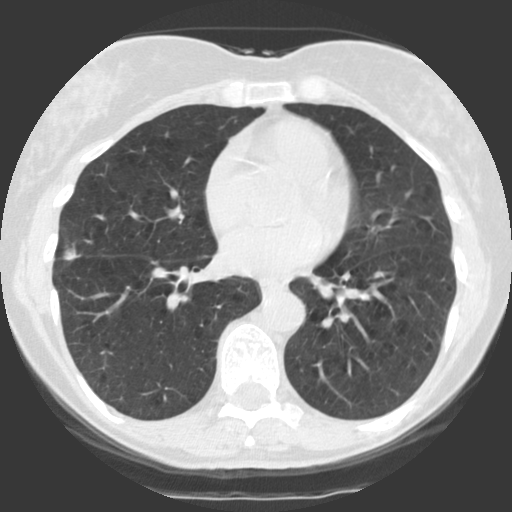
Axial slice from a low-dose chest CT screening exam. Baseline screening round. Lung window (W 1500 / L -600 HU). 2.5 mm slice thickness. Slice 55 of 123 in the series. 512 × 512 image matrix, field of view 290 × 290 mm. Female participant, aged 68 years at enrolment. Former smoker at enrolment.
Expert reader's lesion annotation, bounding box [x1, y1, x2, y2] px = [50, 232, 95, 279]. The screening reader recorded 2 non-calcified nodules or masses ≥4 mm on this exam; which of them this box marks is not recorded. Lung cancer was diagnosed 40 days after this screen: bronchiolo-alveolar adenocarcinoma, NOS, right upper lobe, right middle lobe, right lower lobe, well differentiated (G1), stage IV (AJCC 6th edition).